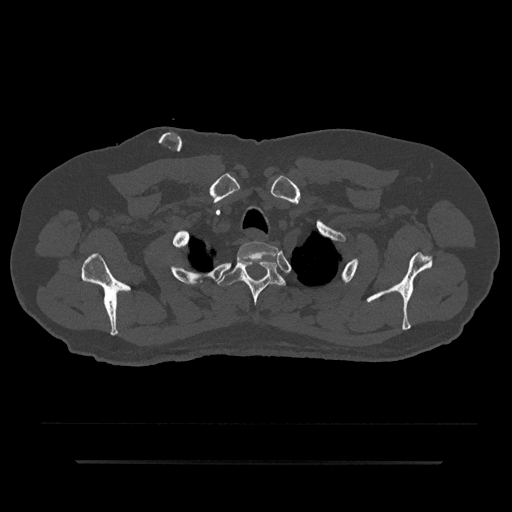
CT including the spine, one axial slice; position 707 of 797 along the scan axis; reconstruction kernel Br40s/3; 120 kVp; bone window (W 1800 / L 400 HU); 0.5 mm slice thickness; 512 × 512 image matrix, field of view 464 × 464 mm. Male patient, age 59 years. Case-level facts recorded for this patient, not image findings: primary cancer: bile ducts; vertebrae with lytic lesions (as recorded): T10.
Annotated regions visible in this slice (semi-automatically segmented with operator editing):
- T1 vertebra: bounding box <236,242,278,263> (left, top, right, bottom; pixels)
- T2 vertebra: <218,257,286,306>